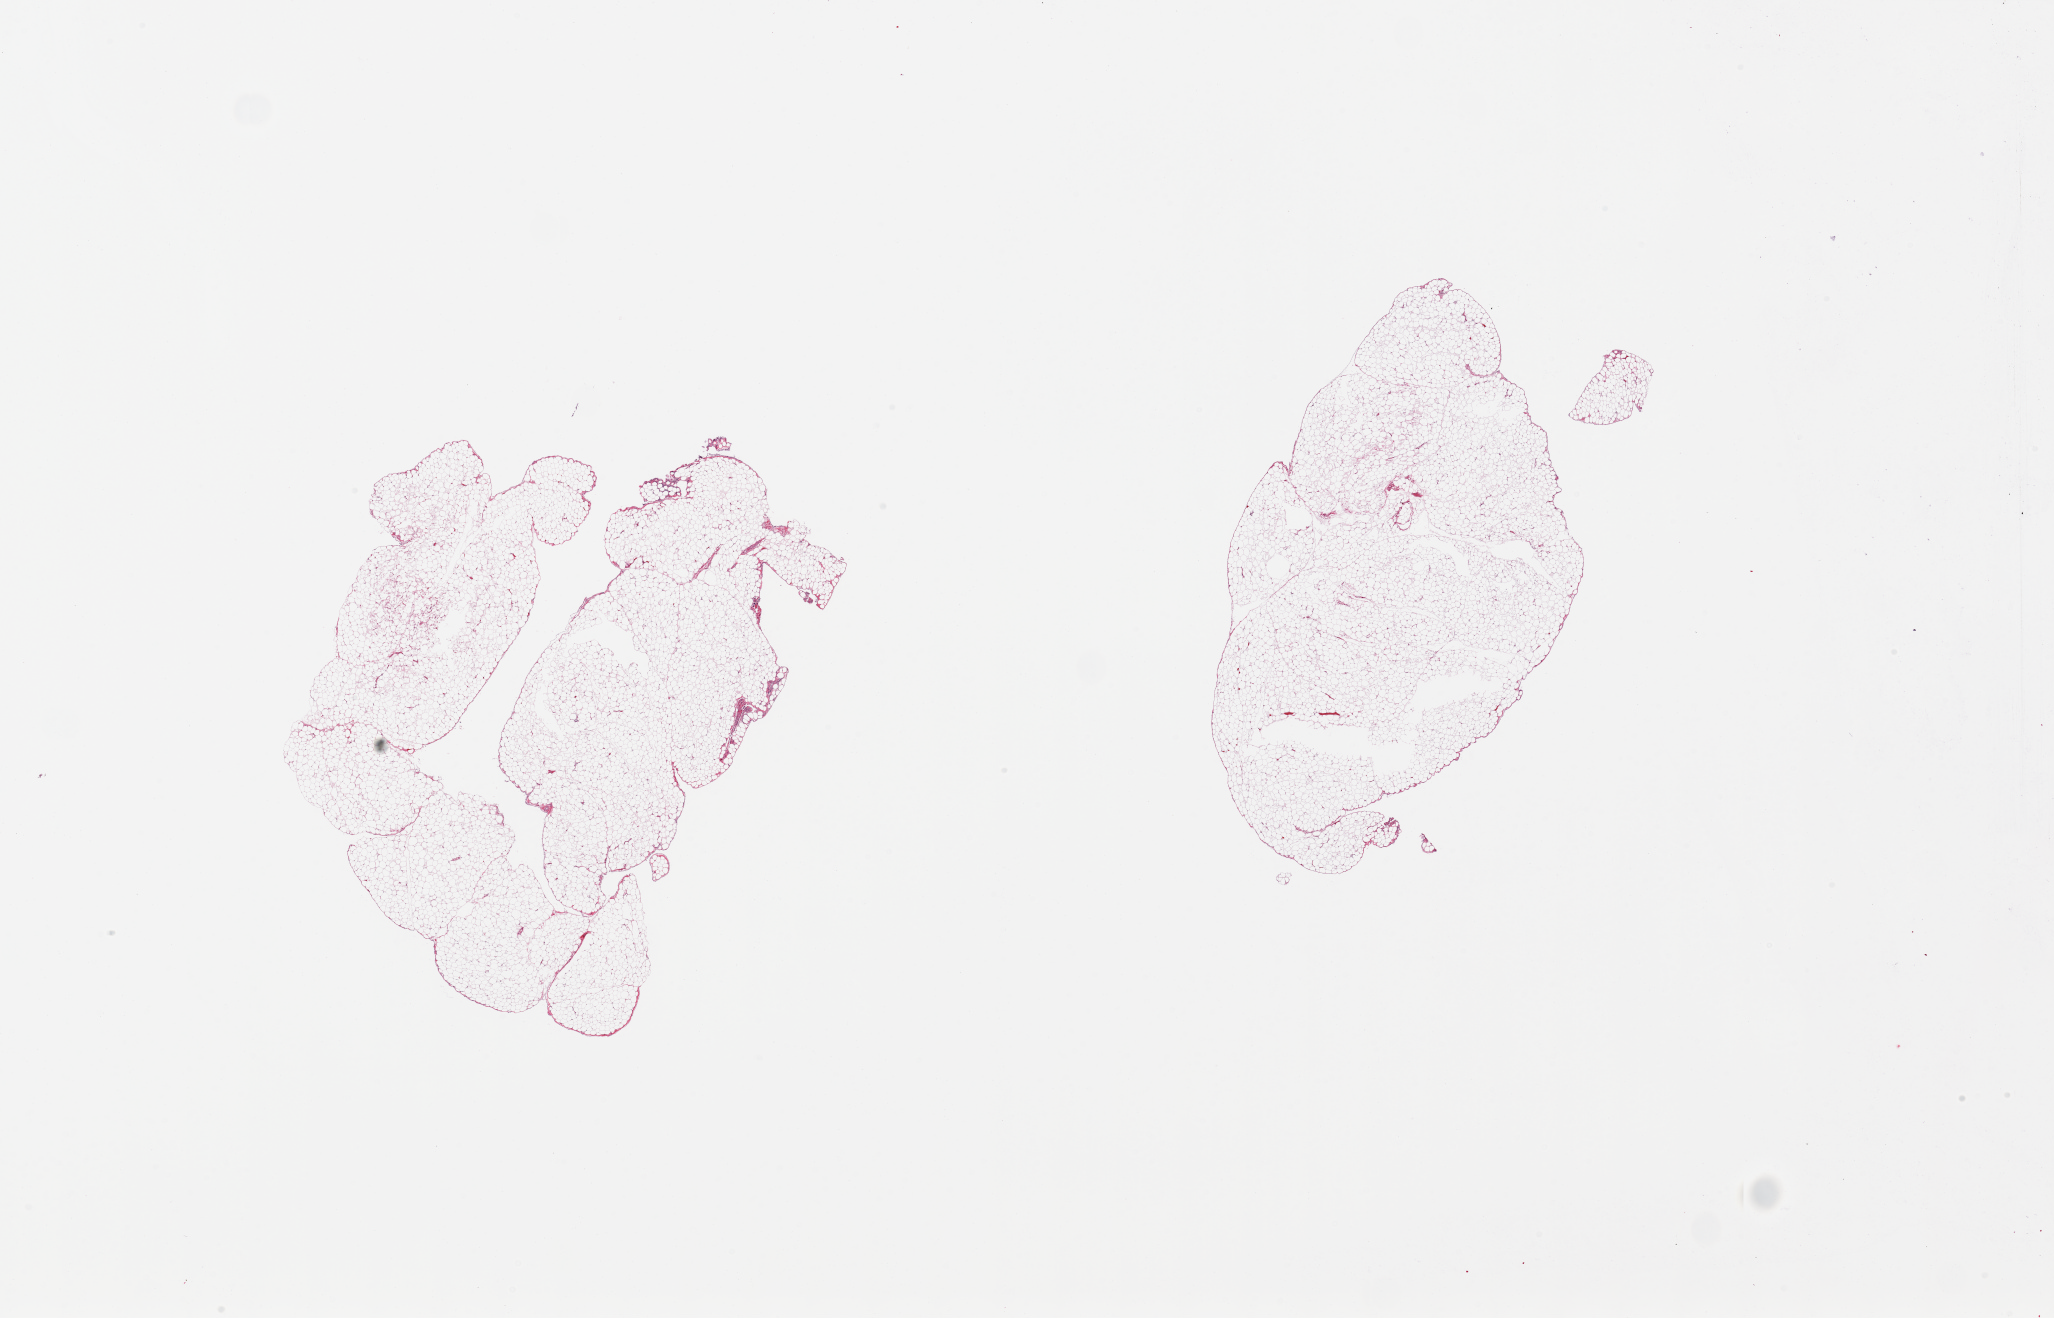
Whole-slide image, hematoxylin and eosin (H&E) stain — whole scanned area (about 32.5 x 20.8 mm) shown as a low-resolution overview; PAXgene-fixed paraffin-embedded (PFPE) section; section of omentum (target tissue); donor tissue sample. Donor: male.
- reviewer comment on this tissue sample: 2 pieces, trace fascia